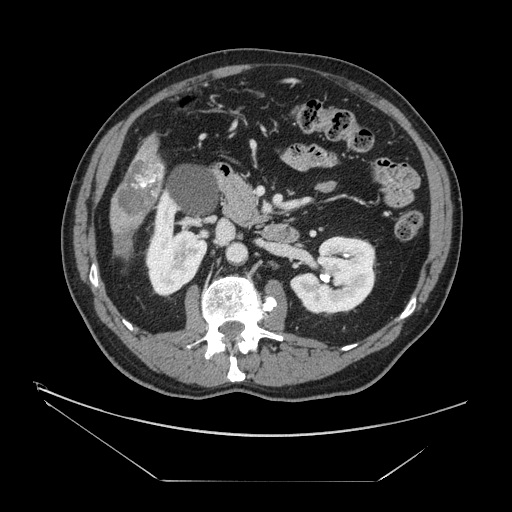
Contrast-enhanced abdominal CT, one axial slice; position 57 of 161 along the scan axis; reconstruction kernel STANDARD; 120 kVp; intravenous contrast given; soft-tissue window (W 400 / L 40 HU); 2.5 mm slice thickness; 512 × 512 image matrix, field of view 440 × 440 mm. Male patient, age 65 years. From the clinical record (not read from this slice): diagnosis: colorectal cancer liver metastases, imaged before liver resection; multiple liver metastases: yes; largest metastasis: 4.2 cm; disease in both lobes: yes.
Annotated regions visible in this slice (outlined manually by an expert reader):
- liver: bounding box <111,138,164,237> (left, top, right, bottom; pixels)
- portal vein (with intrahepatic branches): <136,170,161,188>
- liver metastasis: <114,231,131,255>
- liver metastasis: <117,160,165,217>